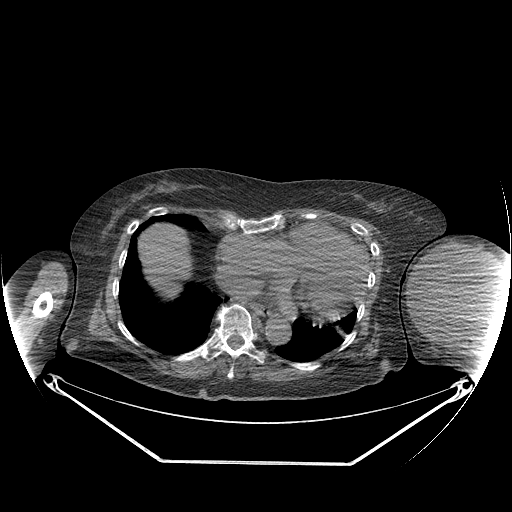
CT of an extremity soft-tissue mass (from a PET/CT study), one axial slice; position 153 of 267 along the scan axis; reconstruction kernel STANDARD; soft-tissue window (W 400 / L 40 HU); 512 × 512 image matrix. Female patient. Case-level facts recorded for this patient, not image findings: histological type: pleiomorphic leiomyosarcoma; grade: high; site of the primary tumour: left biceps.
Outlined on this slice (expert contour drawn on MRI and transferred to this co-registered scan by the dataset authors):
- gross tumour volume including surrounding oedema: bounding box <409,244,499,330> (left, top, right, bottom; pixels)
- gross tumour volume (mass): <409,244,499,327>